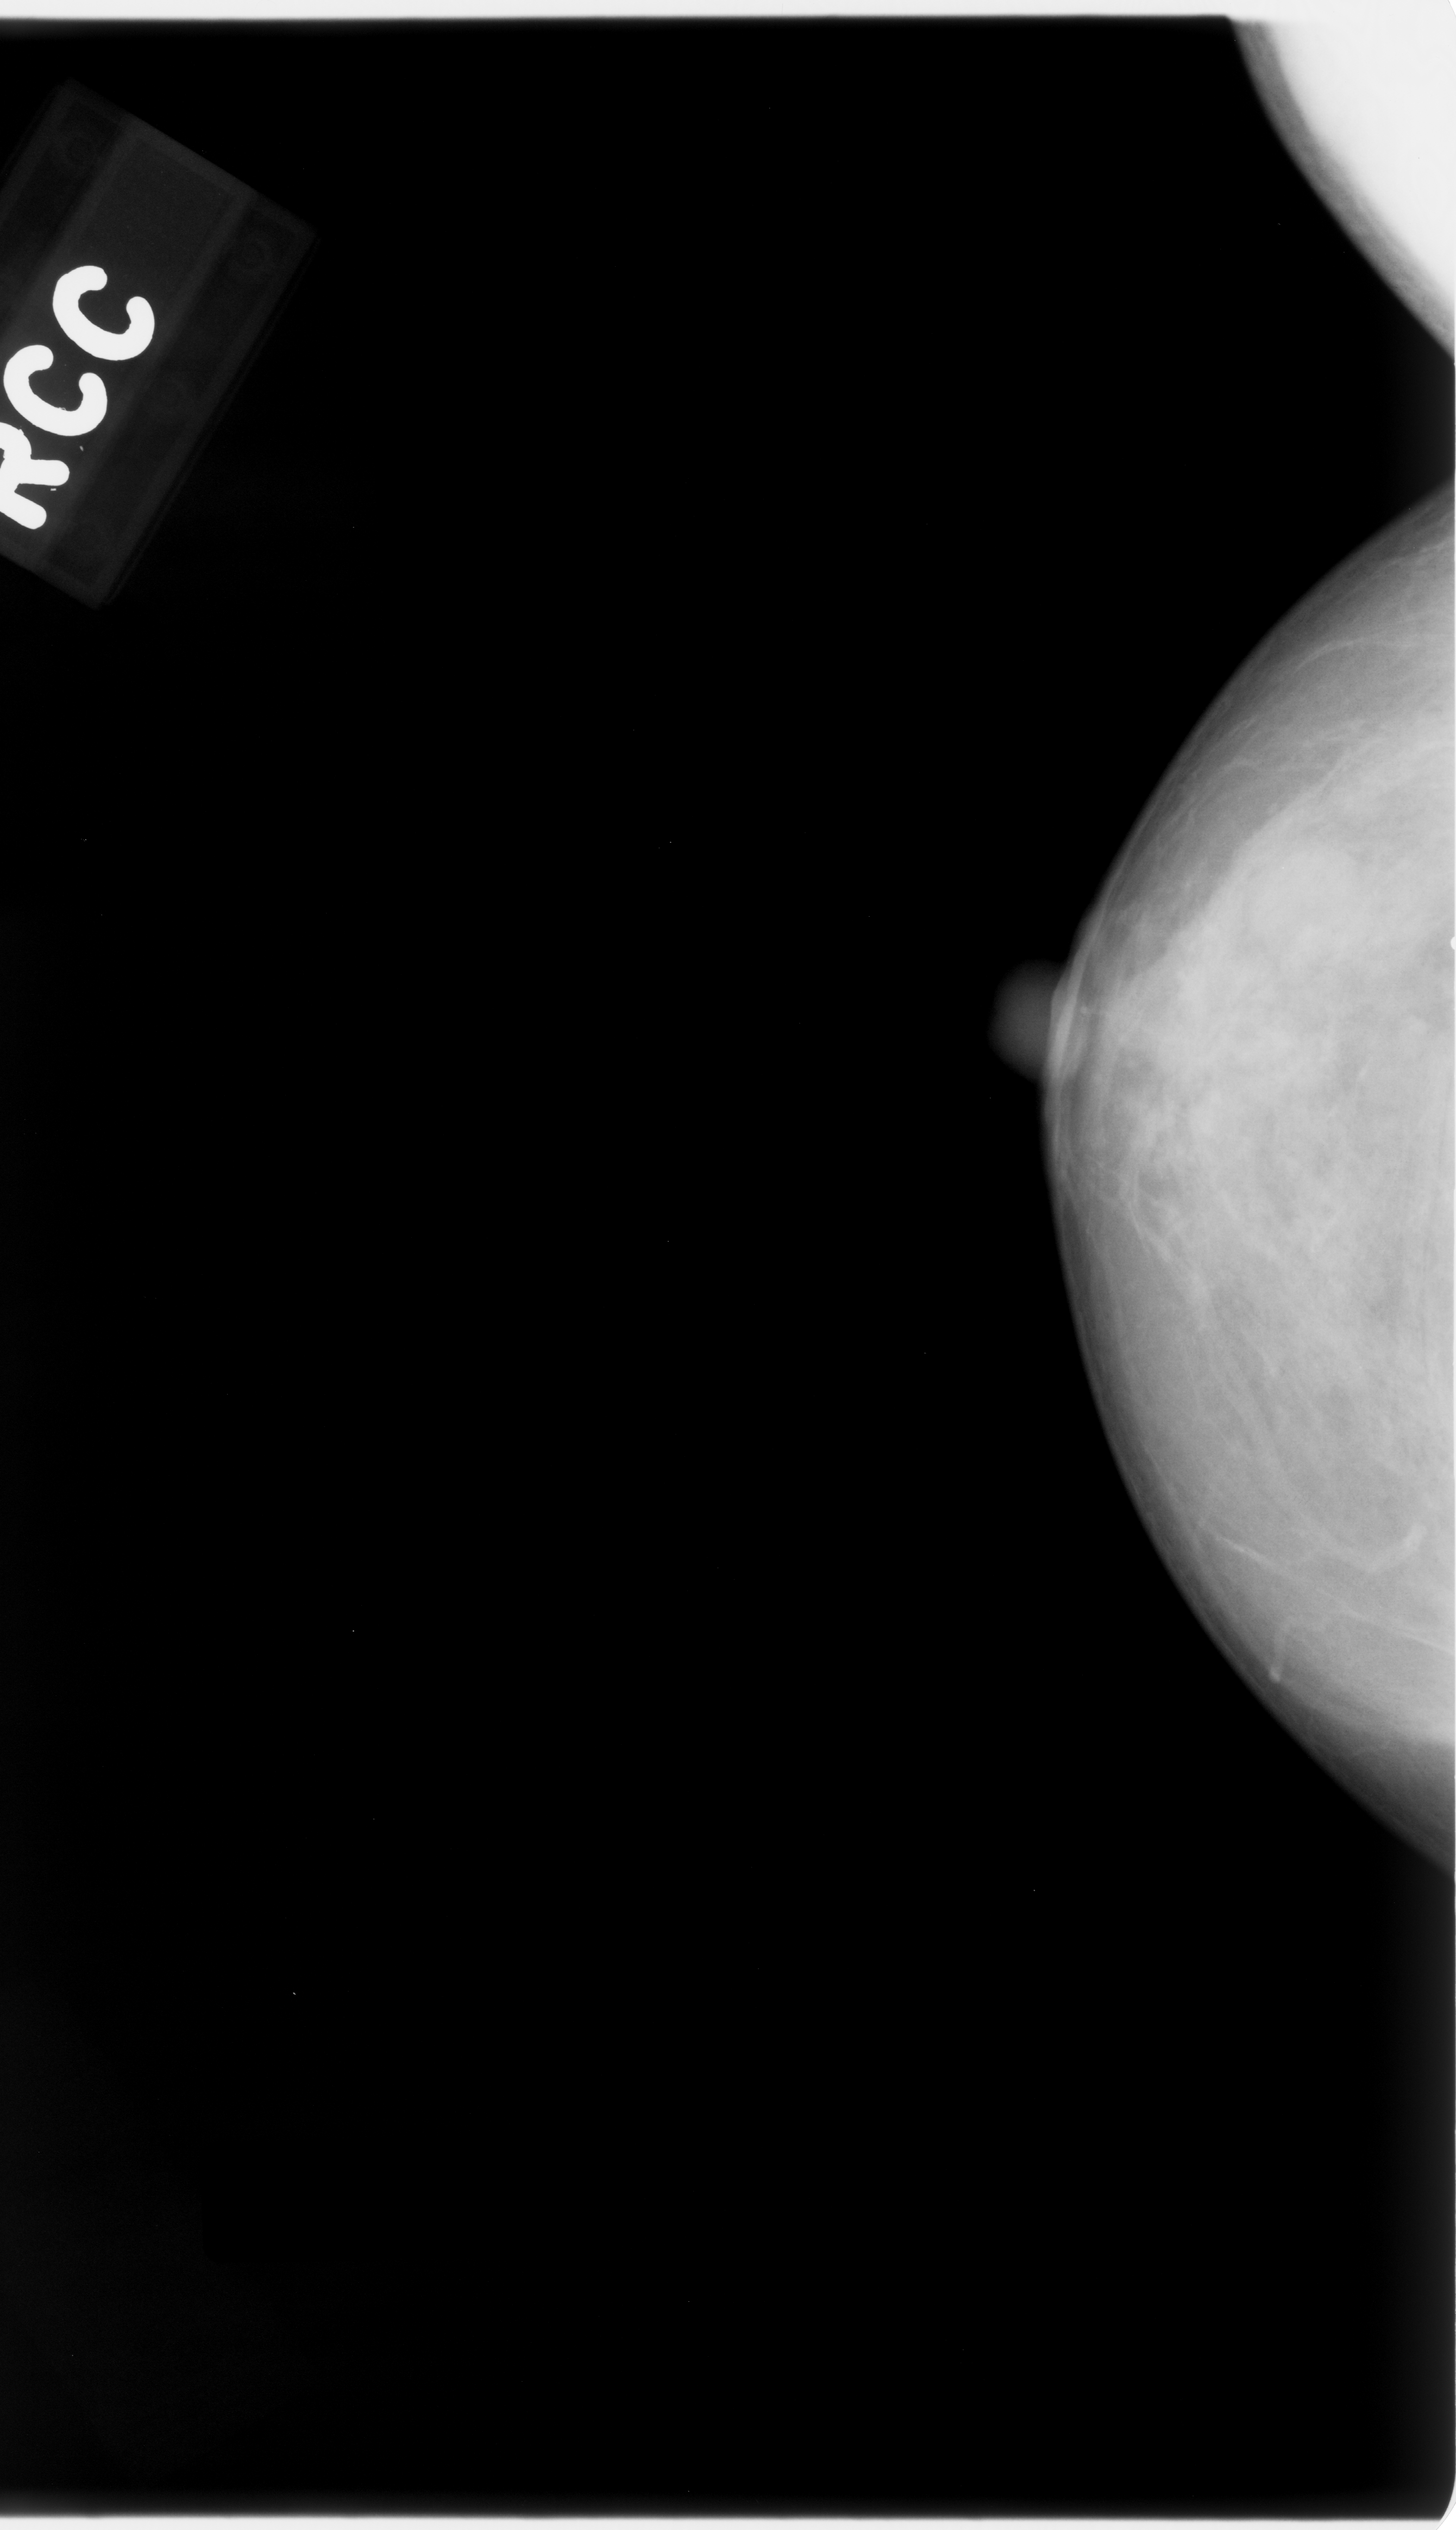
Mammogram (digitized film), right breast, CC view, breast composition: heterogeneously dense (BI-RADS density category 3 of 4).
Finding: mass, shape oval, margins microlobulated; BI-RADS assessment category 4; pathology result (as recorded, not read from the image): benign.